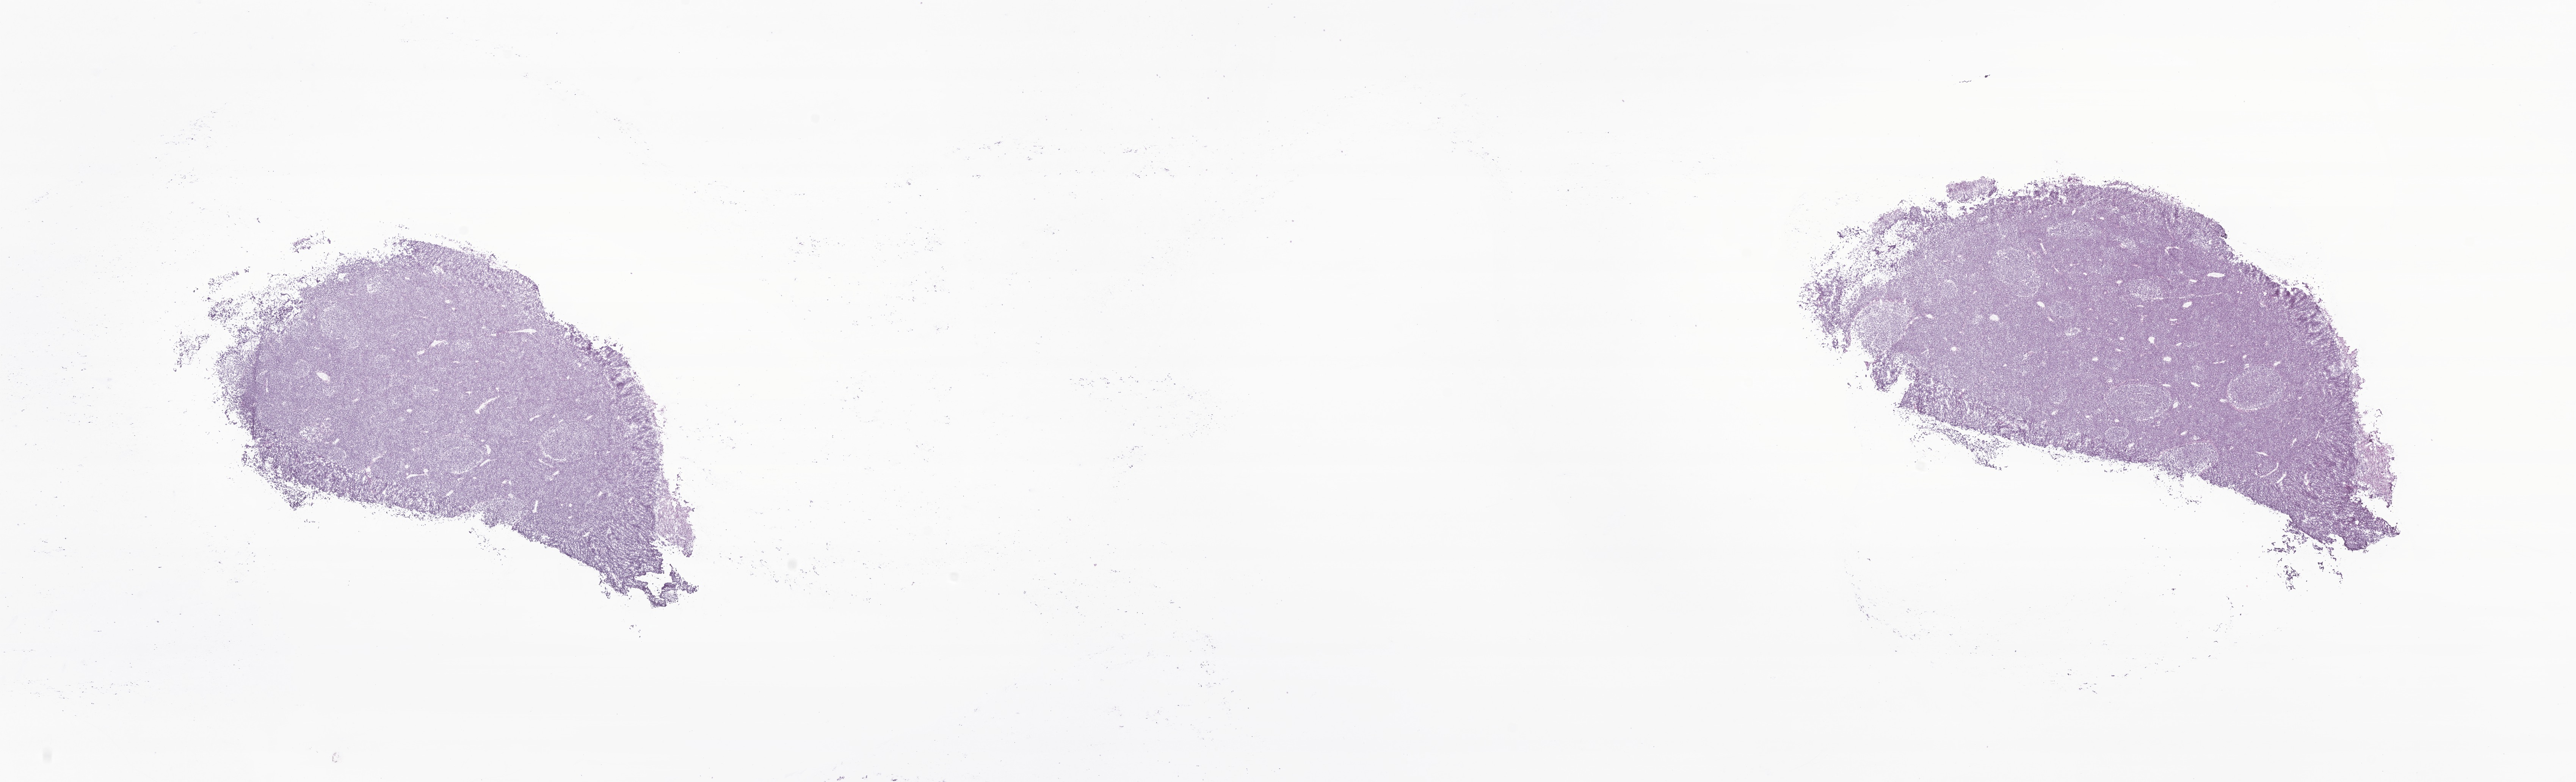
H&E whole-slide image of tumor tissue from the brain — whole scanned area (about 28.7 x 8.7 mm) shown as a low-resolution overview; frozen section. Female patient, age 667 days (about 1.8 years).
Diagnosis (ICD-O-3 morphology term): Medulloblastoma, NOS.